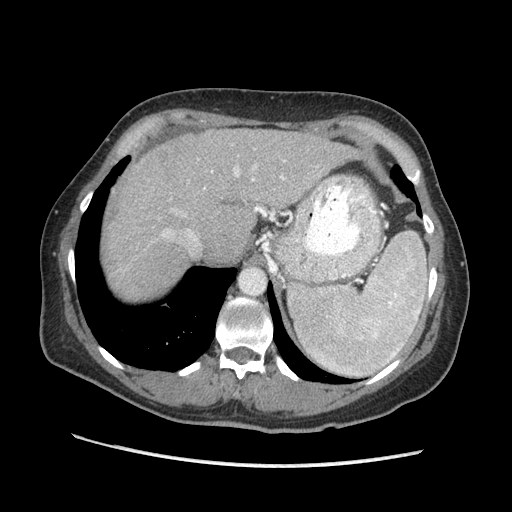
Contrast-enhanced abdominal CT (liver protocol), one axial slice; slice 146 of 170 in the series (ordered by position); 140 kVp; soft-tissue window (W 400 / L 40 HU); 2.5 mm slice thickness; 512 × 512 image matrix, field of view 360 × 360 mm. From the clinical record (not read from this slice): diagnosis: hepatocellular carcinoma (patient treated with transarterial chemoembolisation; whether this scan precedes or follows treatment is not stated here); TNM stage (as recorded): Stage-II; Child-Pugh class: A; tumour nodularity: multinodular; tumour size: 4 cm.
Structures marked on this image (semi-automatic segmentation, software-assisted and operator-edited):
- abdominal aorta: bounding box <240,268,264,295> (left, top, right, bottom; pixels)
- liver parenchyma outside the tumour (the mass and vessels are separate outlines, so this box may not span the whole liver): <106,128,360,298>
- liver vessels: <162,161,286,241>